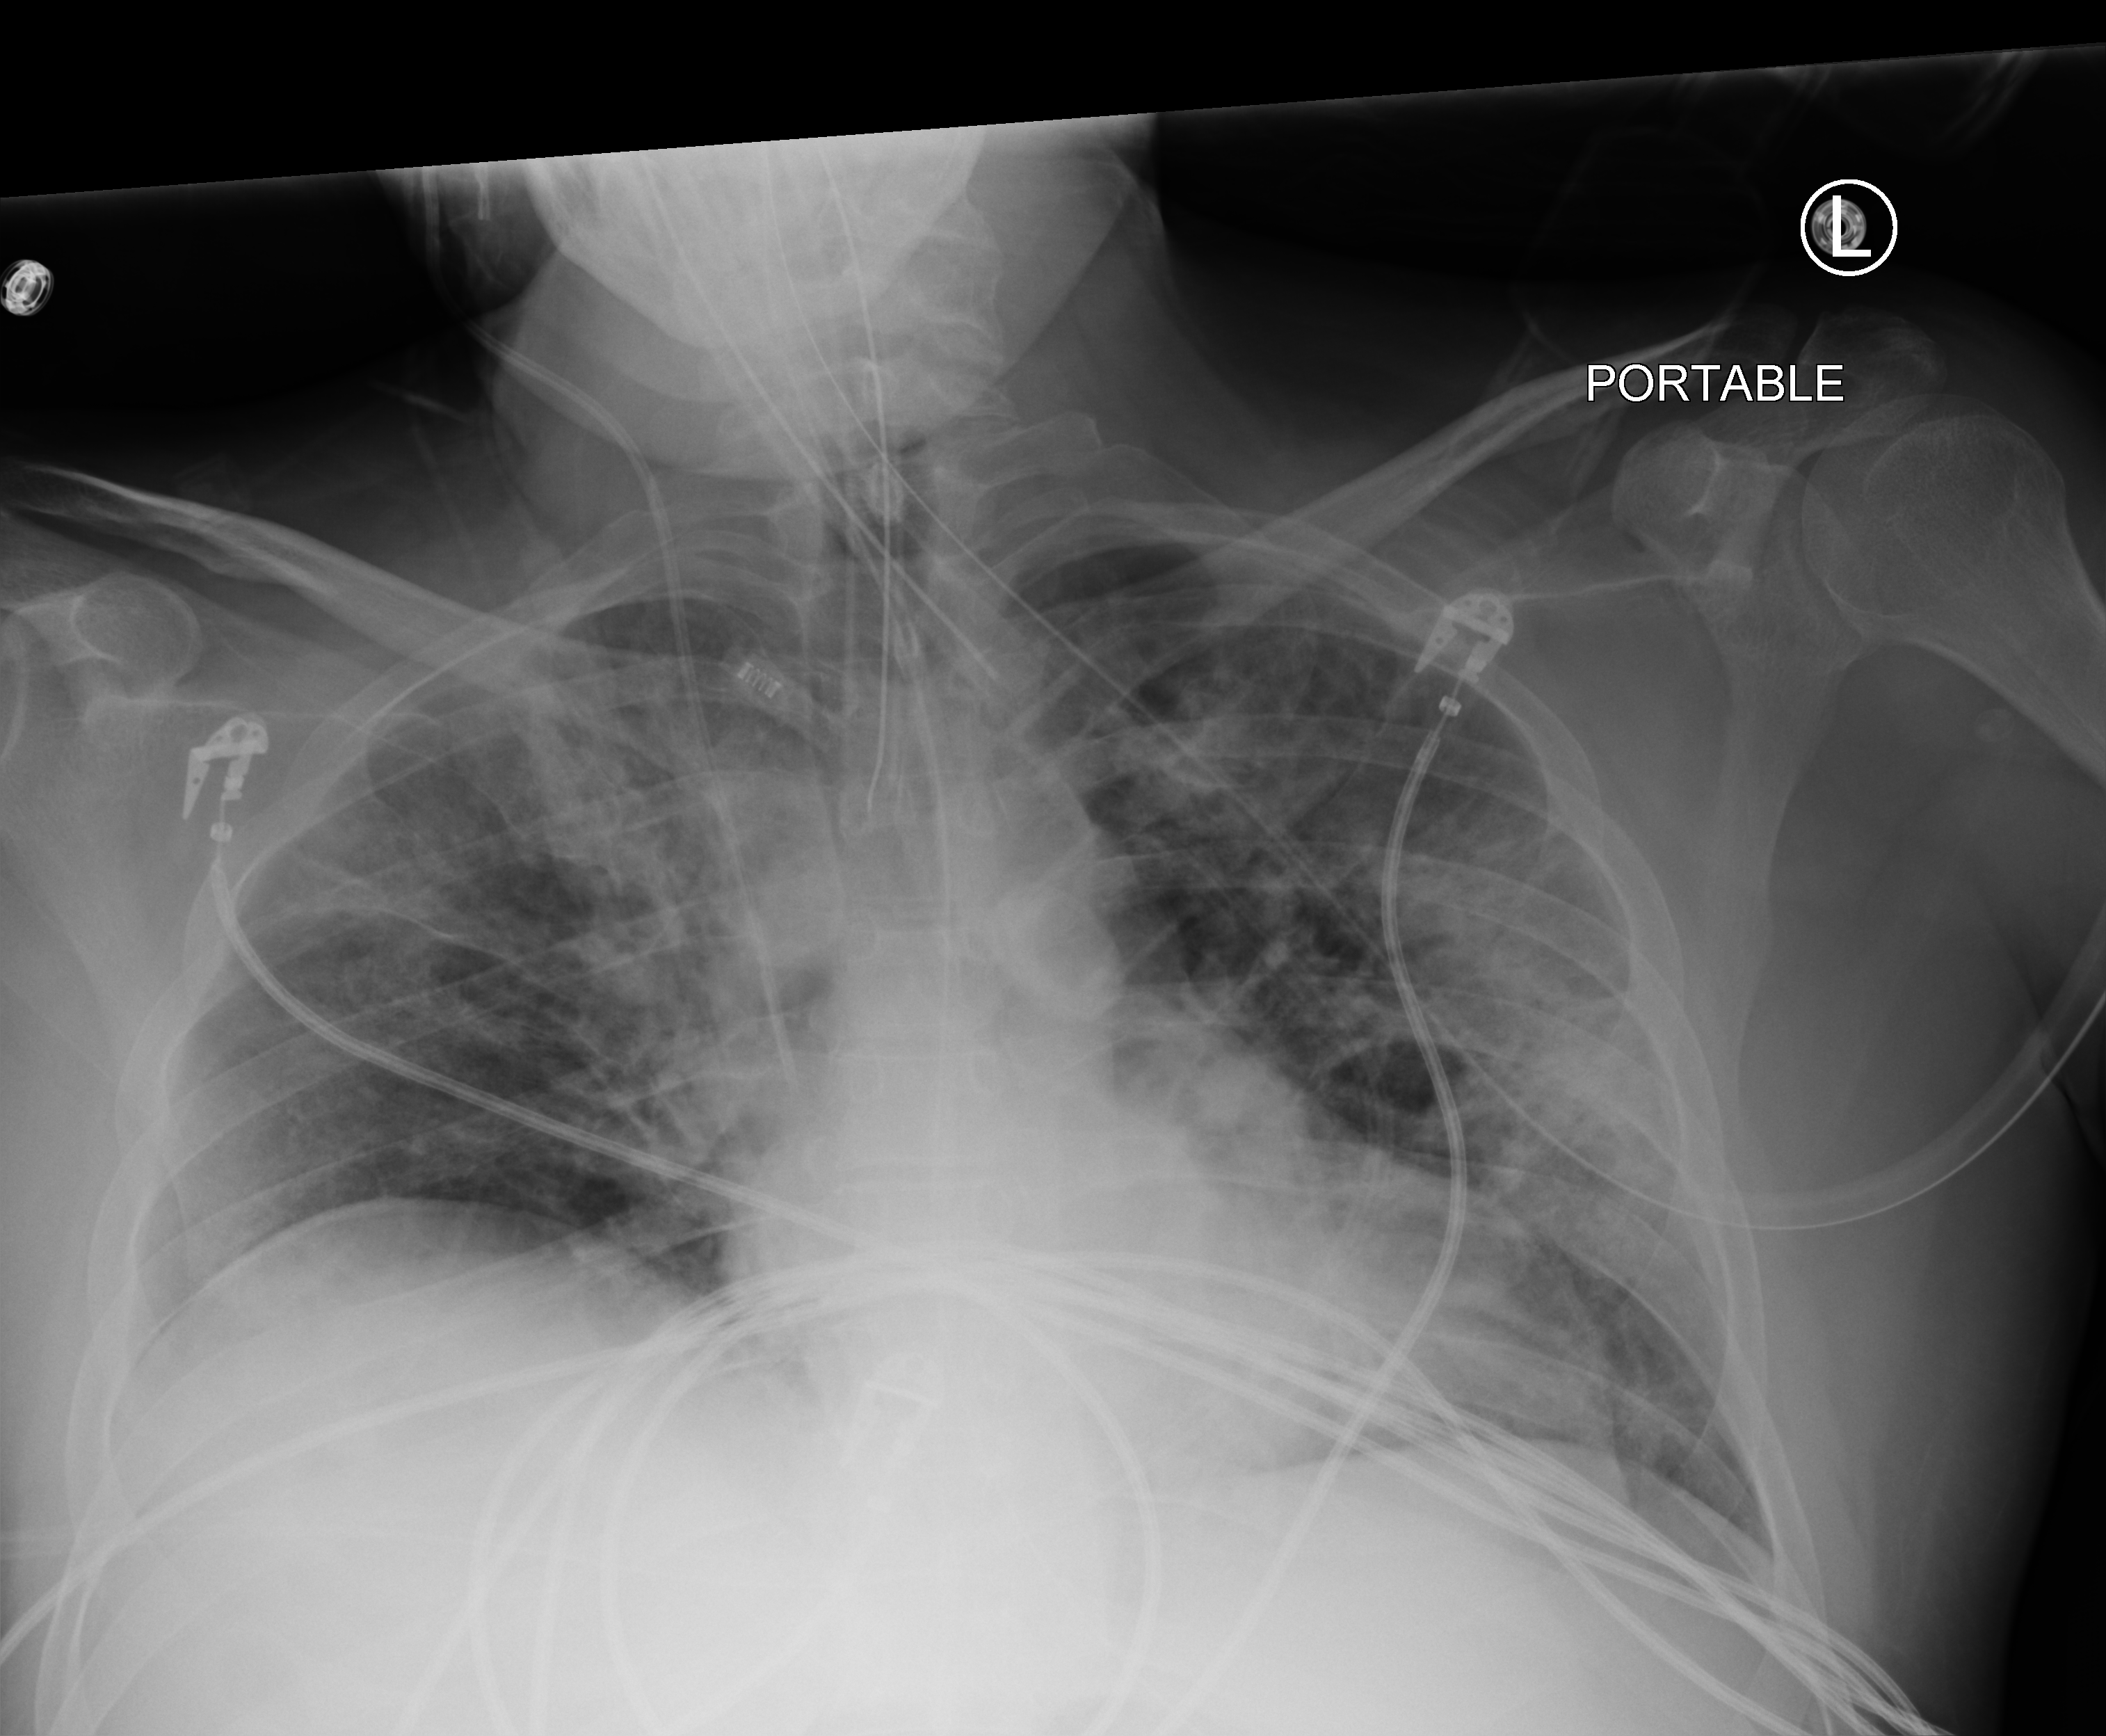
Chest X-ray (portable), anteroposterior (AP) projection. Patient hospitalised with COVID-19; male, aged 18–59 years.
Hospital-stay facts (about this admission, not read from this image; timing relative to this image not recorded): mechanically ventilated during this hospital stay: yes; admitted to intensive care during this hospital stay: yes.